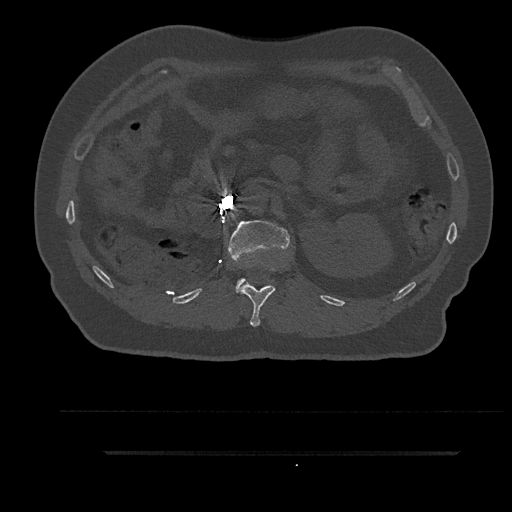
CT including the spine, one axial slice. Position 210 of 797 along the scan axis. 120 kVp. Bone window (W 1800 / L 400 HU). 512 × 512 image matrix, field of view 432 × 432 mm. Male patient, age 63 years. Case-level facts recorded for this patient, not image findings: primary cancer: renal; vertebrae with lytic lesions (as recorded): T8.
Outlined on this slice (semi-automatic segmentation, software-assisted and operator-edited):
- L1 vertebra: bounding box [x1, y1, x2, y2] px = [228, 220, 289, 293]
- T12 vertebra: [239, 266, 276, 327]